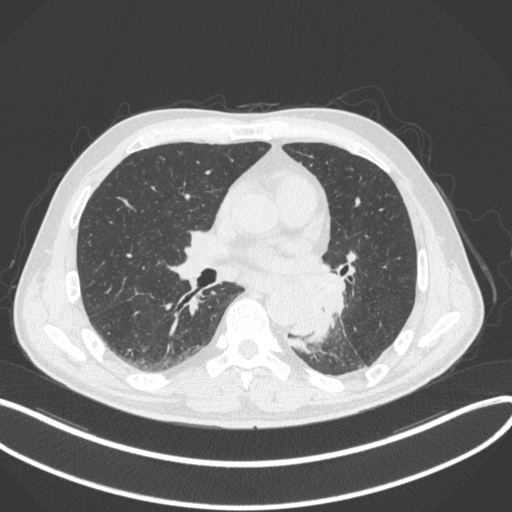
Chest CT, one axial slice. Position 169 of 328 along the scan axis. 120 kVp. Lung window (W 1500 / L -600 HU). 1 mm slice thickness. 512 × 512 image matrix. Patient: male, 59 years. Case-level facts recorded for this patient, not image findings: clinical TNM (as recorded): T2a N2 M0.
Outlined on this slice (rectangle marked by the reading radiologist):
- lung tumour (recorded histology: squamous cell carcinoma): box from (x=287, y=273) to (x=348, y=344) px